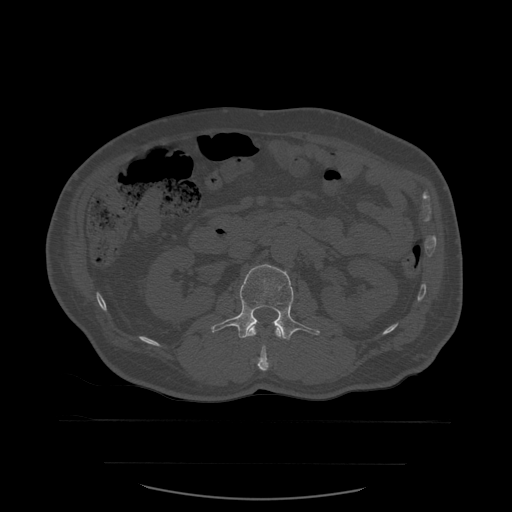
CT including the spine, one axial slice. Slice 226 of 590 in the series (ordered by position). Bone window (W 1800 / L 400 HU). 1.25 mm slice thickness. 512 × 512 image matrix, field of view 479 × 479 mm. Patient age 71 years. Case-level facts recorded for this patient, not image findings: primary cancer: lung.
Outlined on this slice (semi-automatically segmented with operator editing):
- L1 vertebra: bounding box (x1, y1, x2, y2) in pixels: (248, 327, 282, 371)
- L2 vertebra: (211, 264, 320, 340)